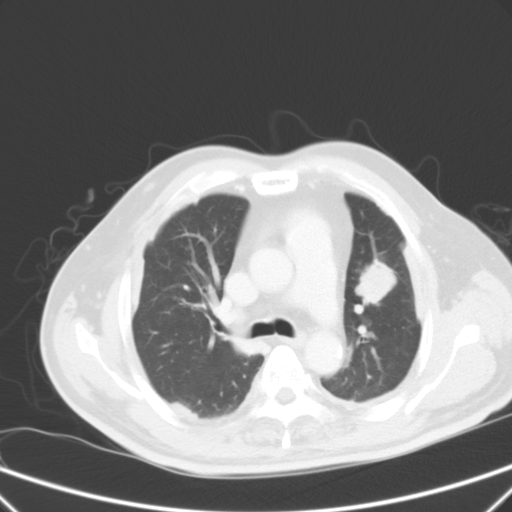
Chest CT, one axial slice. Slice 39 of 59 in the series (ordered by position). Intravenous contrast given. Lung window (W 1500 / L -600 HU). 5 mm slice thickness. 512 × 512 image matrix, field of view 357 × 357 mm. Male patient, age 66 years. From the clinical record (not read from this slice): clinical TNM (as recorded): T1c N3 M1a.
Structures marked on this image (bounding box drawn by a radiologist):
- lung tumour (recorded histology: squamous cell carcinoma): bounding box (x1, y1, x2, y2) in pixels: (351, 253, 401, 308)